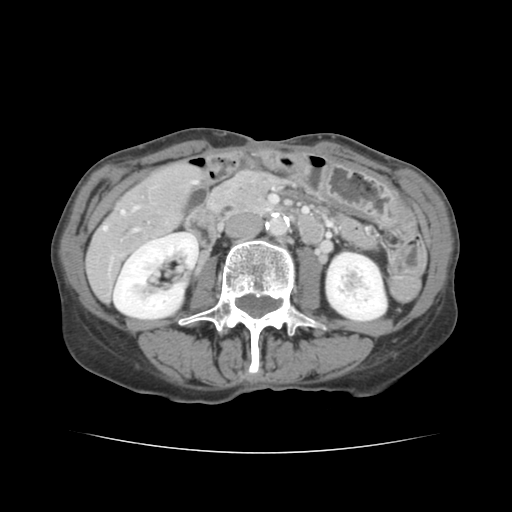
Contrast-enhanced abdominal CT, one axial slice. Intravenous contrast given. Soft-tissue window (W 400 / L 40 HU). 512 × 512 image matrix, field of view 319 × 319 mm. Female patient, age 77 years. From the clinical record (not read from this slice): diagnosis: colorectal cancer liver metastases, imaged before liver resection.
Outlined on this slice (outlined manually by an expert reader):
- hepatic veins: bounding box [x1, y1, x2, y2] px = [104, 181, 196, 230]
- liver: [88, 164, 202, 298]
- planned liver remnant (the part of the liver to remain after resection): [173, 164, 201, 187]
- portal vein (with intrahepatic branches): [134, 229, 139, 231]